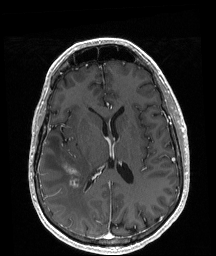
Brain MRI from a brain-tumour surgery series, one axial slice. Position 94 of 208 along the scan axis. T1-weighted post-contrast. 1 mm slice thickness. 216 × 256 image matrix. From the clinical record (not read from this slice): histopathology: Astrocytoma; WHO grade: 4; IDH mutation: yes; tumour location: Right Temporal.
Annotated regions visible in this slice (manually delineated by an expert):
- tumour: bounding box (x1, y1, x2, y2) in pixels: (66, 168, 79, 187)